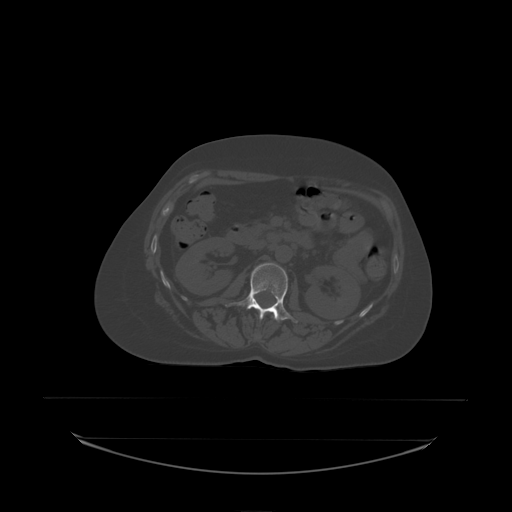
CT including the spine, one axial slice; bone window (W 1800 / L 400 HU); 512 × 512 image matrix, field of view 500 × 500 mm. Female patient, age 53 years. Case-level facts recorded for this patient, not image findings: primary cancer: lung.
Structures marked on this image (semi-automatically segmented with operator editing):
- L1 vertebra: box from (x=272, y=316) to (x=274, y=318) px
- L2 vertebra: (x=226, y=263)–(x=298, y=323)